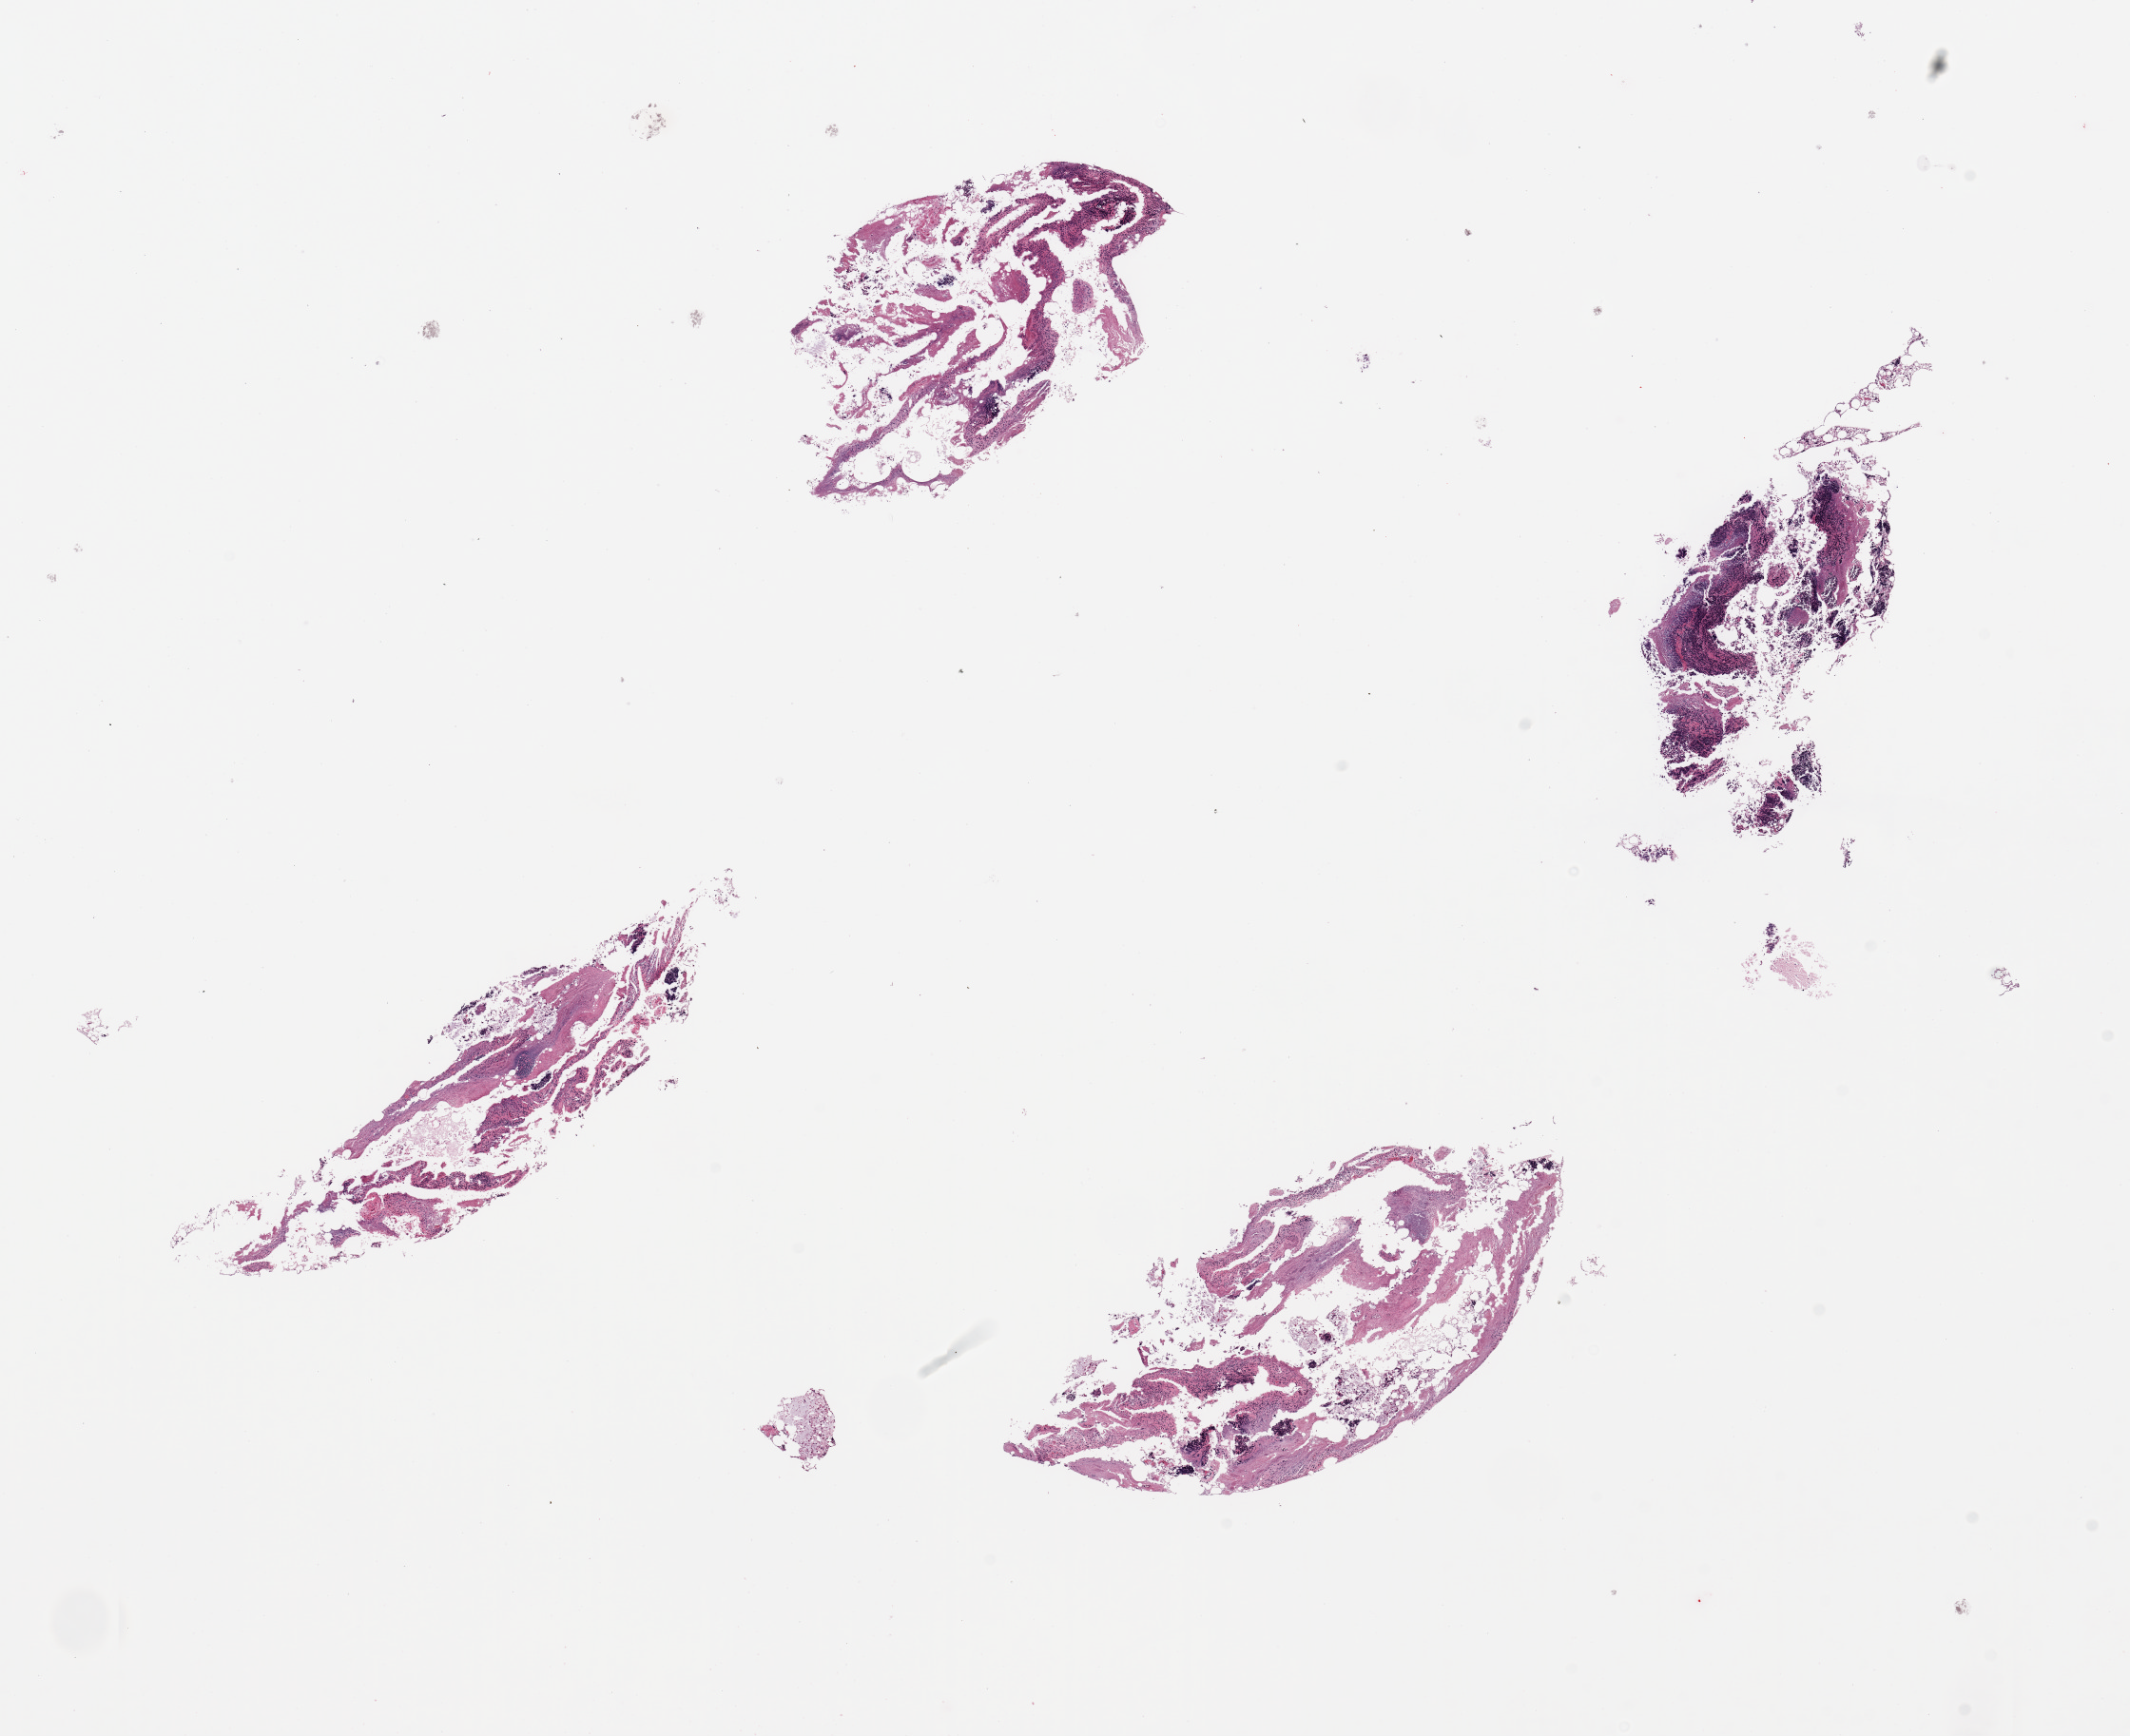
Digitized H&E-stained section, a low-resolution overview of the entire scanned area, about 17.7 x 14.4 mm. PAXgene-fixed paraffin-embedded (PFPE) section. Section of ileum (target tissue). Tissue donor sample. Donor: female.
- pathologist's review note for this sample: 4 pieces; fragments of autolyzed mucosa with focal residual prominent lymphoid elements